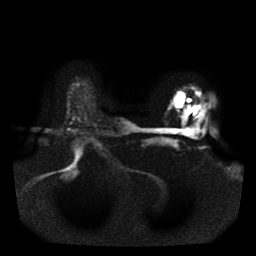
Breast MRI, one axial slice. Position 32 of 41 along the scan axis. Diffusion-weighted series; image 2 of 4 stored at this slice position (different b-values; order by instance number). 1.5 T. 5 mm slice thickness. 256 × 256 image matrix, field of view 330 × 330 mm. Female patient.
Outlined on this slice (outlined manually by an expert reader):
- tumour on diffusion-weighted imaging: bounding box (x1, y1, x2, y2) in pixels: (176, 94, 183, 107)